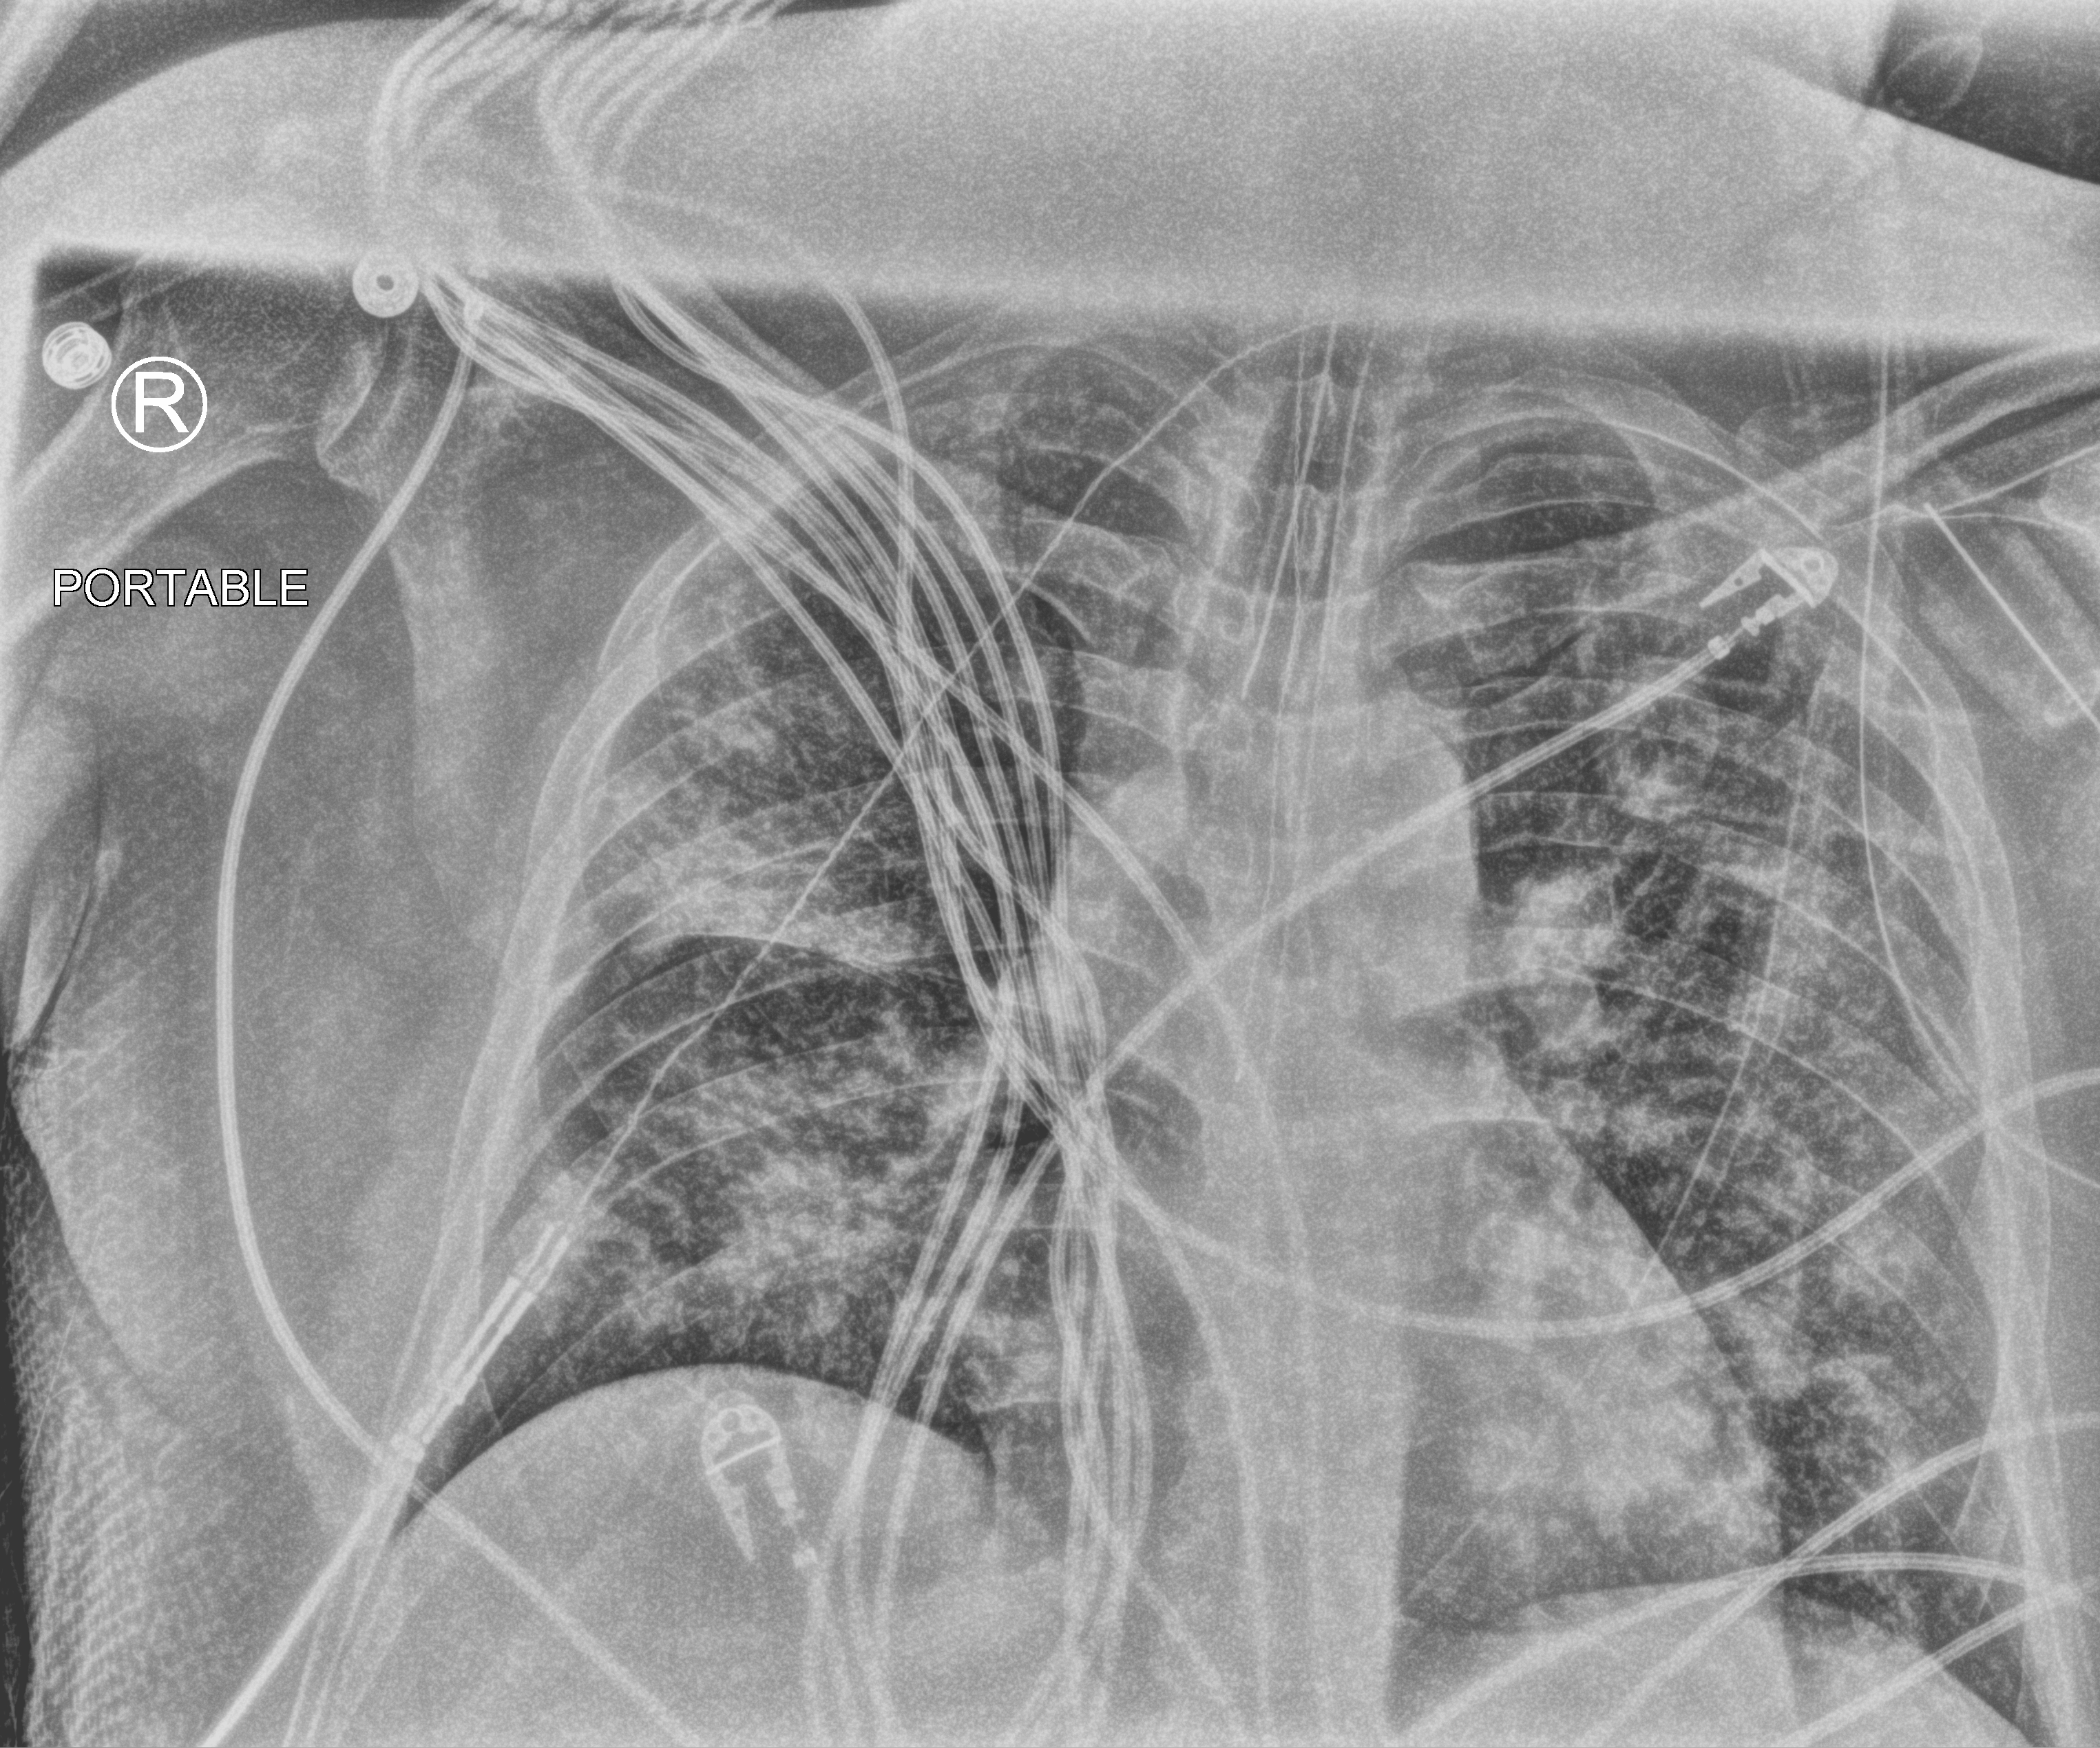
Chest X-ray (portable); anteroposterior (AP) projection. Patient hospitalised with COVID-19, aged 18–59 years.
Hospital-stay facts (about this admission, not read from this image; timing relative to this image not recorded): chronic kidney disease (admission record): no; hypertension (admission record): yes; length of hospital stay: 50 days.